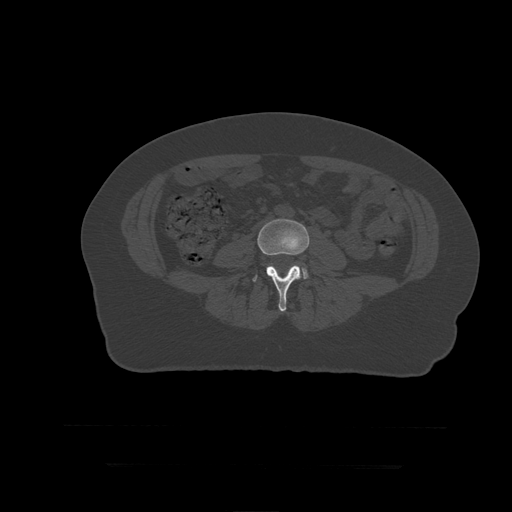
CT including the spine, one axial slice; slice 92 of 399 in the series (ordered by position); reconstruction kernel STANDARD; 120 kVp; bone window (W 1800 / L 400 HU); 1.25 mm slice thickness; 512 × 512 image matrix, field of view 450 × 450 mm. Patient age 41 years. Case-level facts recorded for this patient, not image findings: primary cancer: breast.
Annotated regions visible in this slice (semi-automatic segmentation, software-assisted and operator-edited):
- L4 vertebra: box from (x=253, y=218) to (x=310, y=312) px
- L5 vertebra: (x=300, y=266)–(x=309, y=280)